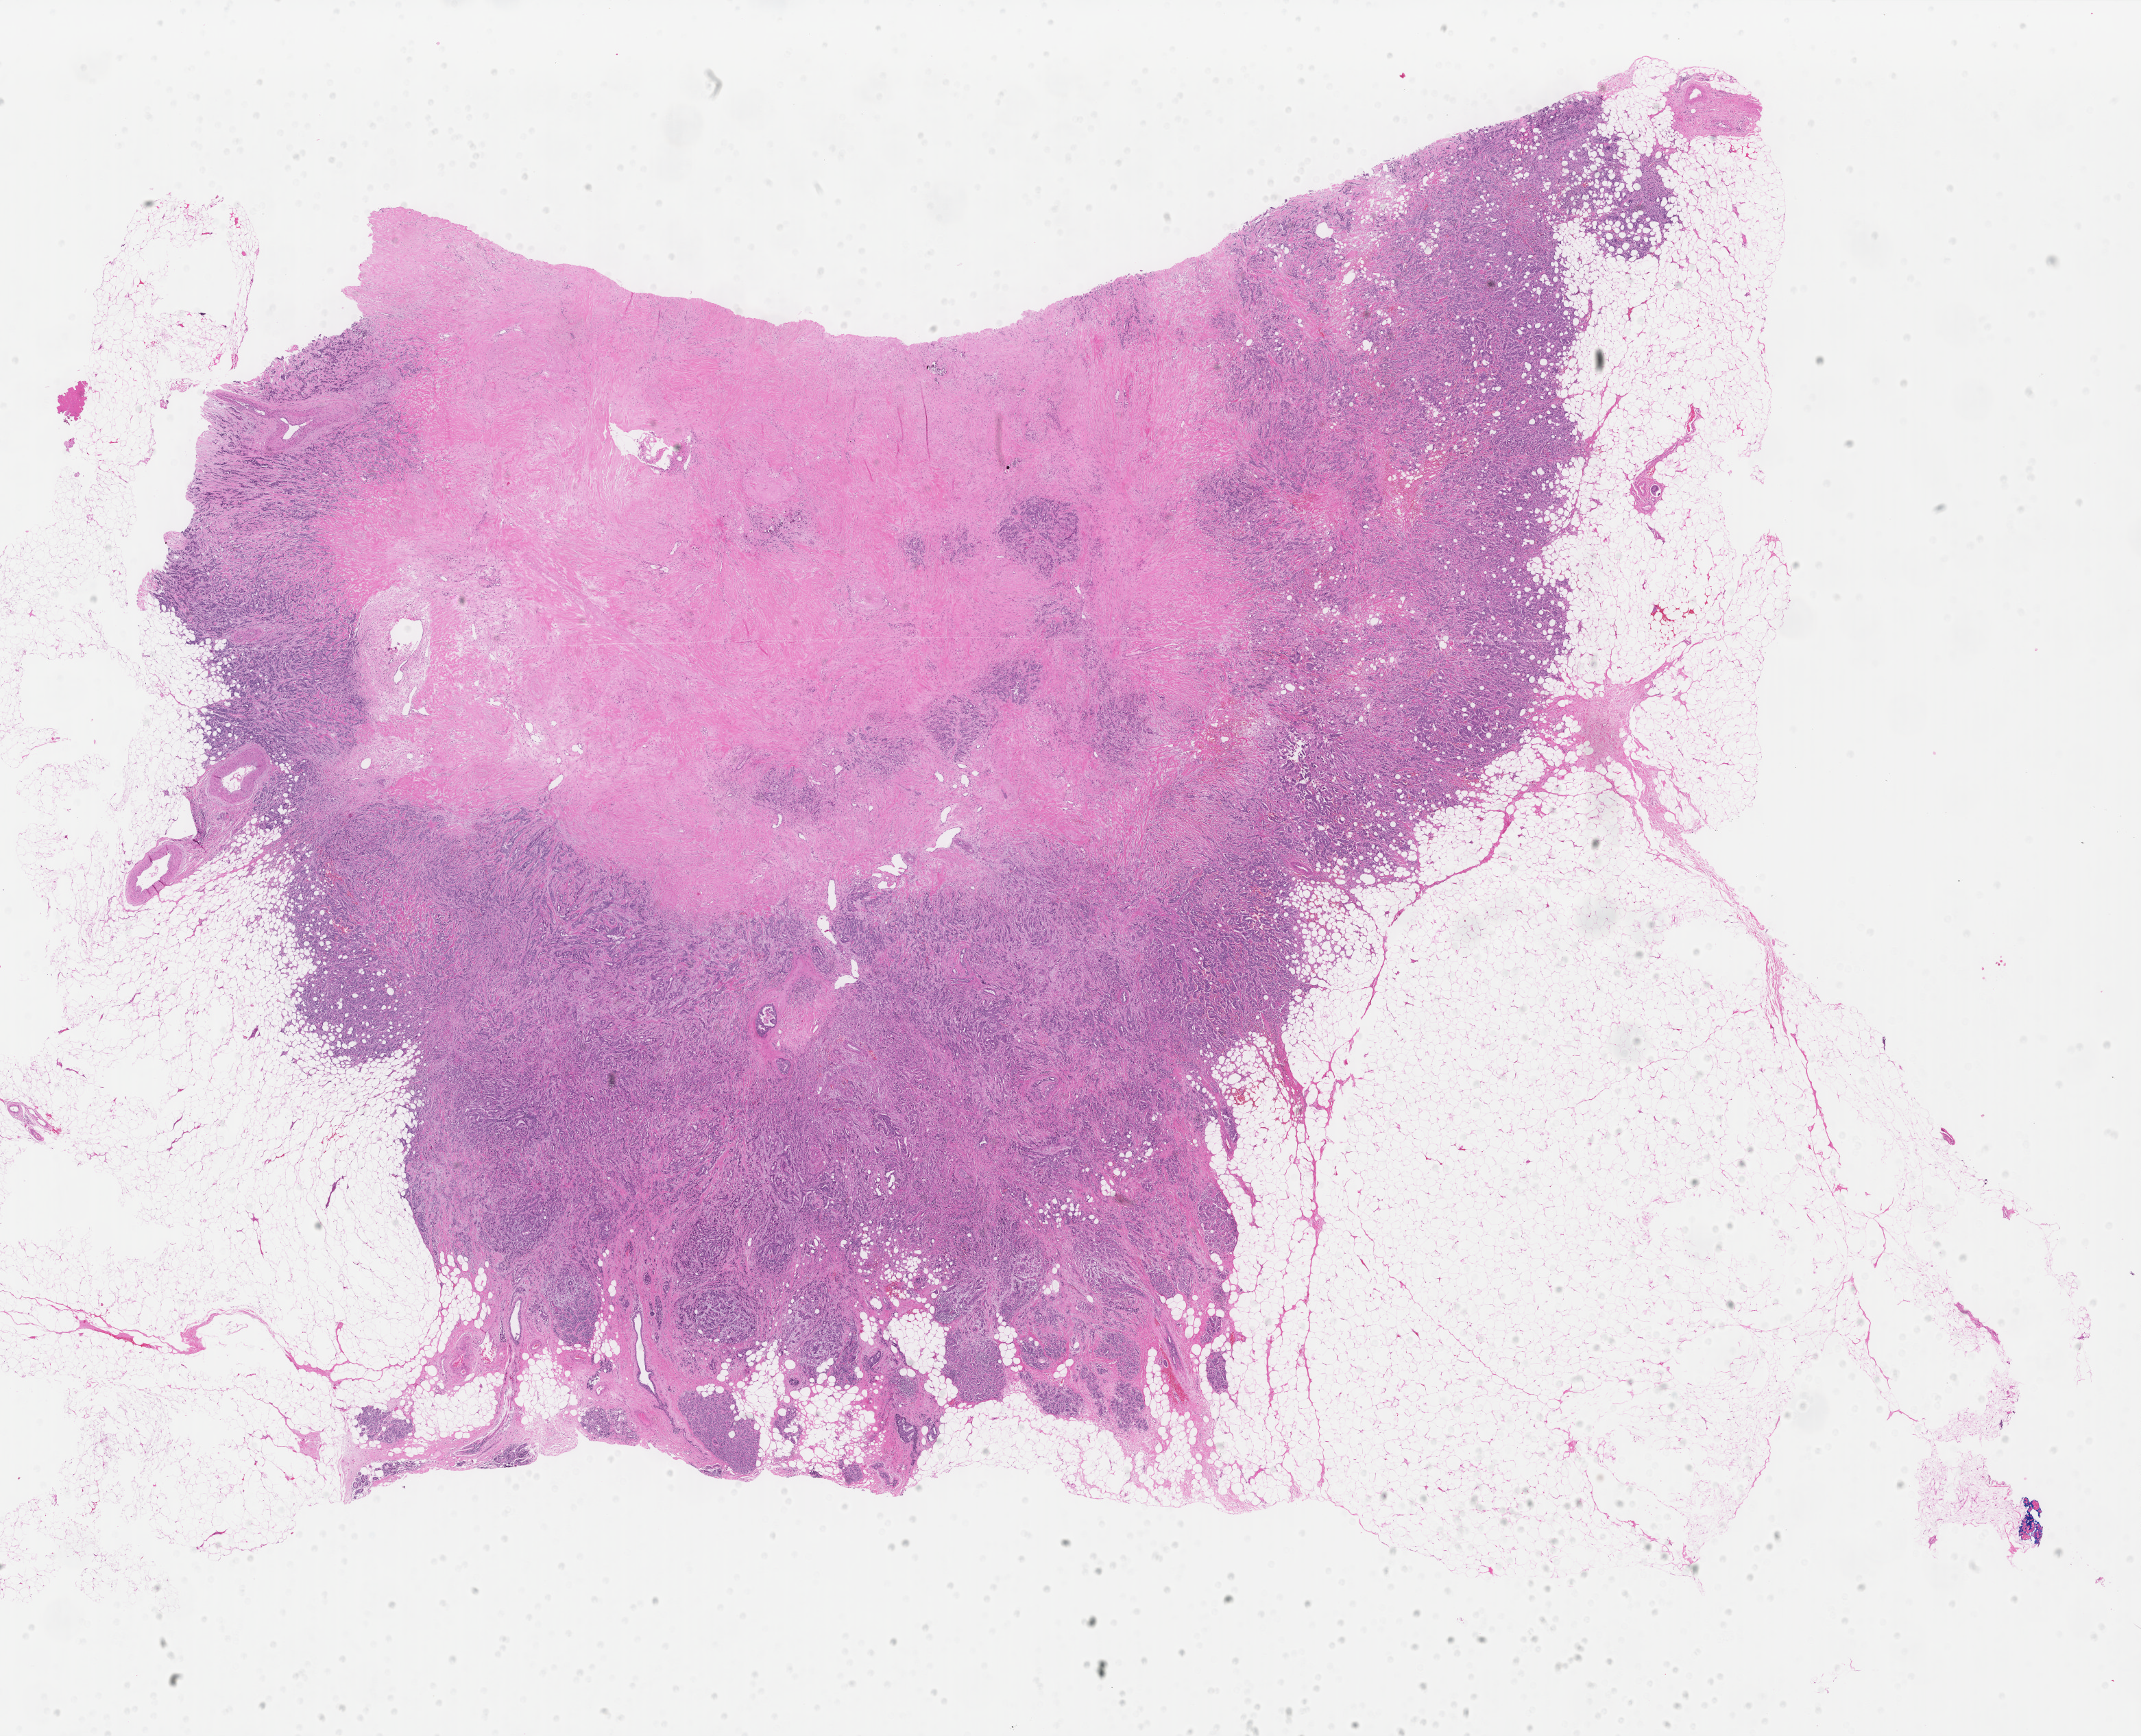
Digitized Hematoxylin and eosin (H&E) stained tissue section (whole slide) — a low-resolution overview of the entire scanned area, about 24.8 x 20.1 mm (slide scanned at 40x); formalin-fixed paraffin-embedded (FFPE) diagnostic section; breast, primary tumour sample. Female, age 51 years at initial diagnosis.
- pathologic diagnosis: Infiltrating duct carcinoma, NOS
- AJCC pathologic stage: IIA